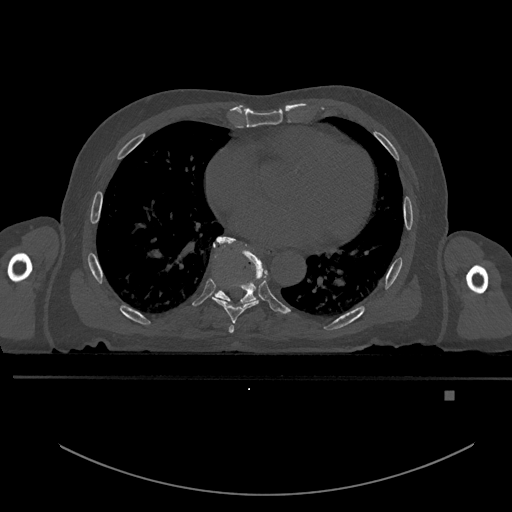
CT including the spine, one axial slice. Position 233 of 969 along the scan axis. Bone window (W 1800 / L 400 HU). 0.5 mm slice thickness. 512 × 512 image matrix, field of view 456 × 456 mm. Patient: male, 82 years. Case-level facts recorded for this patient, not image findings: primary cancer: prostate.
Outlined on this slice (semi-automatically segmented with operator editing):
- T6 vertebra: bounding box [x1, y1, x2, y2] px = [228, 324, 234, 333]
- T7 vertebra: [213, 236, 268, 323]
- T8 vertebra: [212, 239, 262, 307]